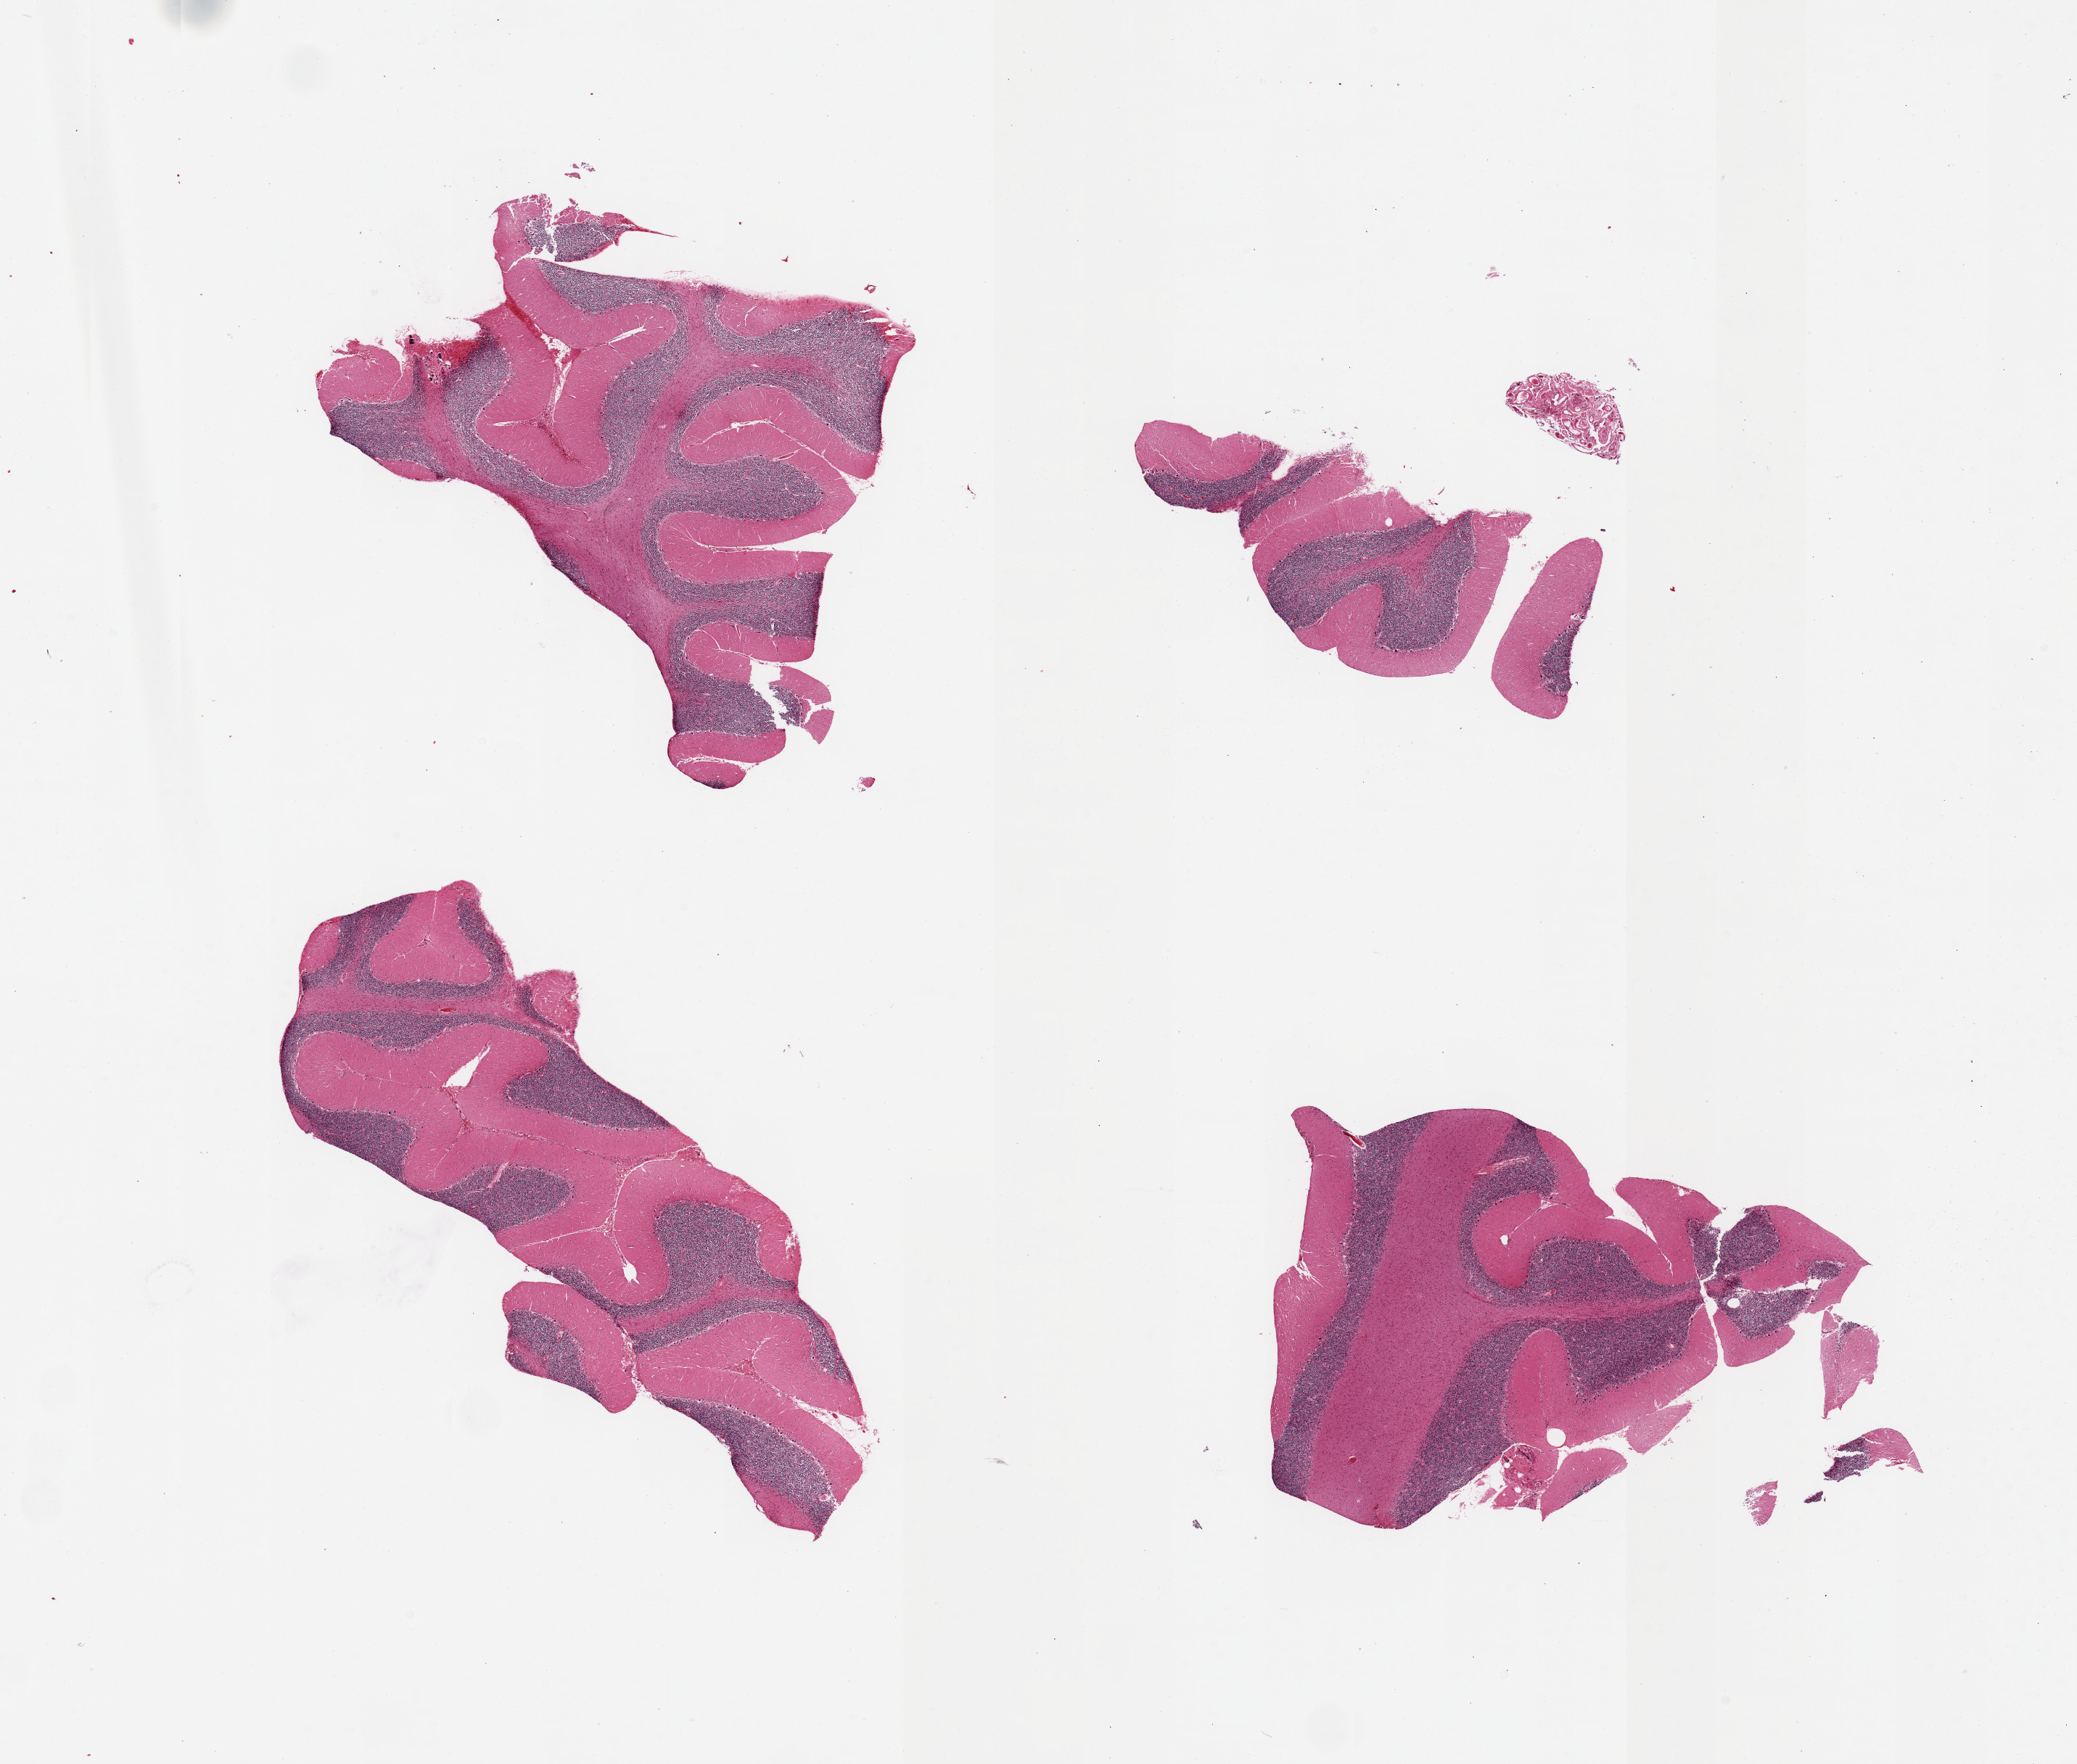
Whole-slide image, H&E stain, low-resolution overview of the scanned area, about 22.6 x 19.2 mm. PAXgene-fixed, paraffin-embedded tissue. Sampled site (target tissue): cerebellum. Donor tissue sample. Donor sex: male.
* pathologist's review note for this sample: 4 pieces, no abnormalities